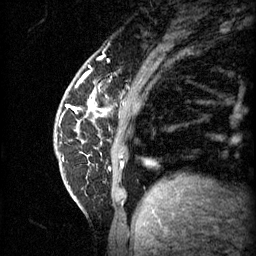
Breast MRI (dynamic contrast-enhanced), one sagittal slice; position 11 of 60 along the scan axis; 3 images stored at this slice position (order not interpretable as contrast timing); 1.5 T; TE 4.2 ms, TR 11 ms; 256 × 256 image matrix, field of view 180 × 180 mm. Patient: female, 62 years.
Outlined on this slice (semi-automatically segmented with operator editing):
- analysis volume of interest (the breast-tissue region the enhancement analysis was run in; not a lesion): bounding box [x1, y1, x2, y2] px = [56, 72, 109, 135]
- tumour enhancement mask (voxels above the 70 % enhancement threshold inside the analysis volume of interest): [76, 100, 97, 111]